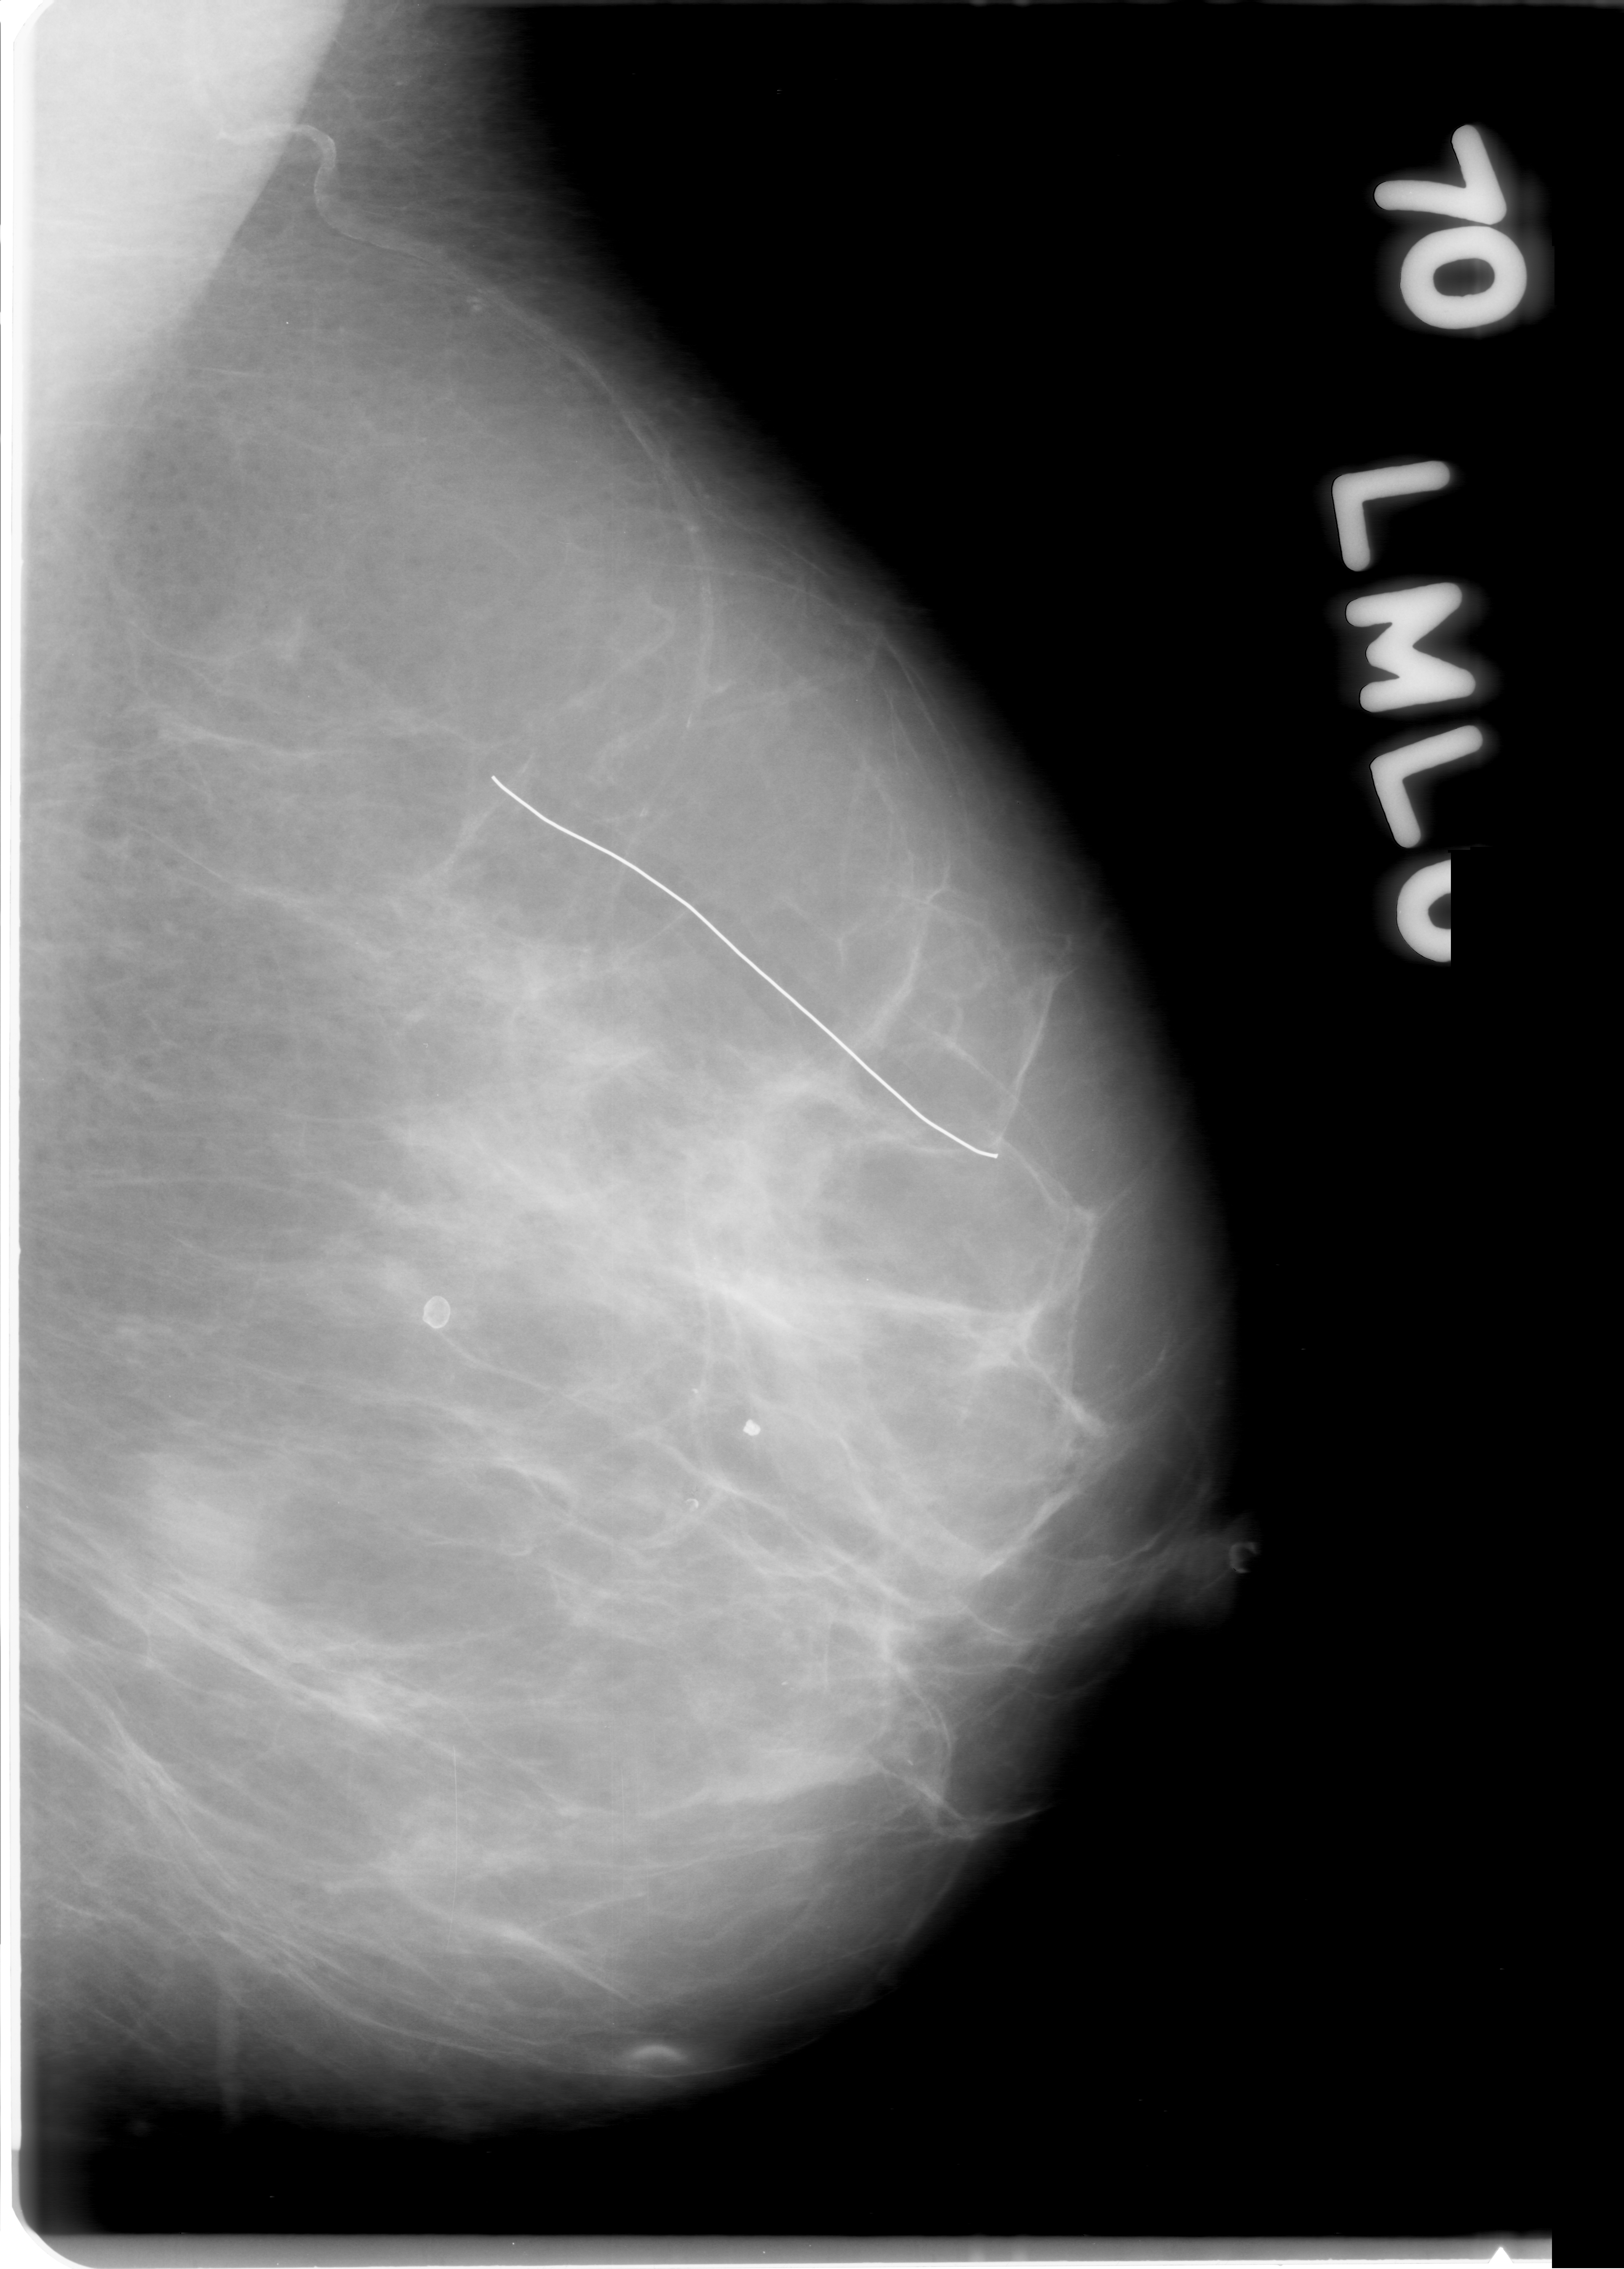
Scanned film-screen mammogram. Left breast. MLO view. BI-RADS breast density category 2 (scale 1–4). 1624 × 2269 image matrix.
Expert-marked regions of interest on this film, with their recorded descriptors:
- mass, shape oval, margins microlobulated; BI-RADS assessment category 0; subtlety rating 5 on a 1 (subtle) to 5 (obvious) scale; pathology (as recorded): benign: bounding box [x1, y1, x2, y2] px = [109, 1406, 296, 1568]